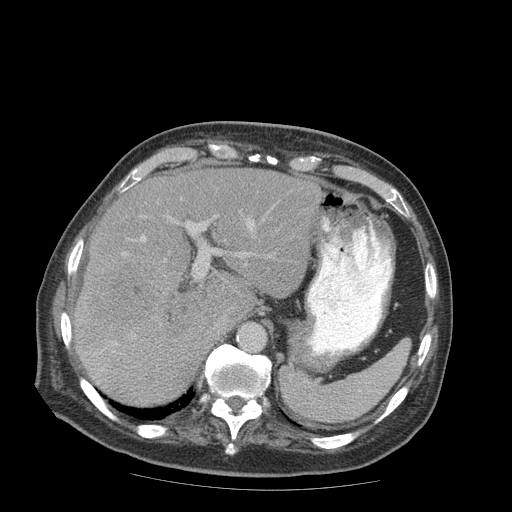
Contrast-enhanced abdominal CT (liver protocol), one axial slice; position 62 of 99 along the scan axis; reconstruction kernel STANDARD; 140 kVp; soft-tissue window (W 400 / L 40 HU); 2.5 mm slice thickness; 512 × 512 image matrix, field of view 420 × 420 mm. Case-level facts recorded for this patient, not image findings: diagnosis: hepatocellular carcinoma (patient treated with transarterial chemoembolisation; whether this scan precedes or follows treatment is not stated here); TNM stage (as recorded): Stage-IIIB; Child-Pugh class: A; tumour differentiation: well differentiated; tumour nodularity: multinodular.
Outlined on this slice (semi-automatic segmentation, software-assisted and operator-edited):
- liver parenchyma outside the tumour (the mass and vessels are separate outlines, so this box may not span the whole liver): bounding box <72,168,322,404> (left, top, right, bottom; pixels)
- mass: <78,267,154,339>
- liver vessels: <100,219,254,353>